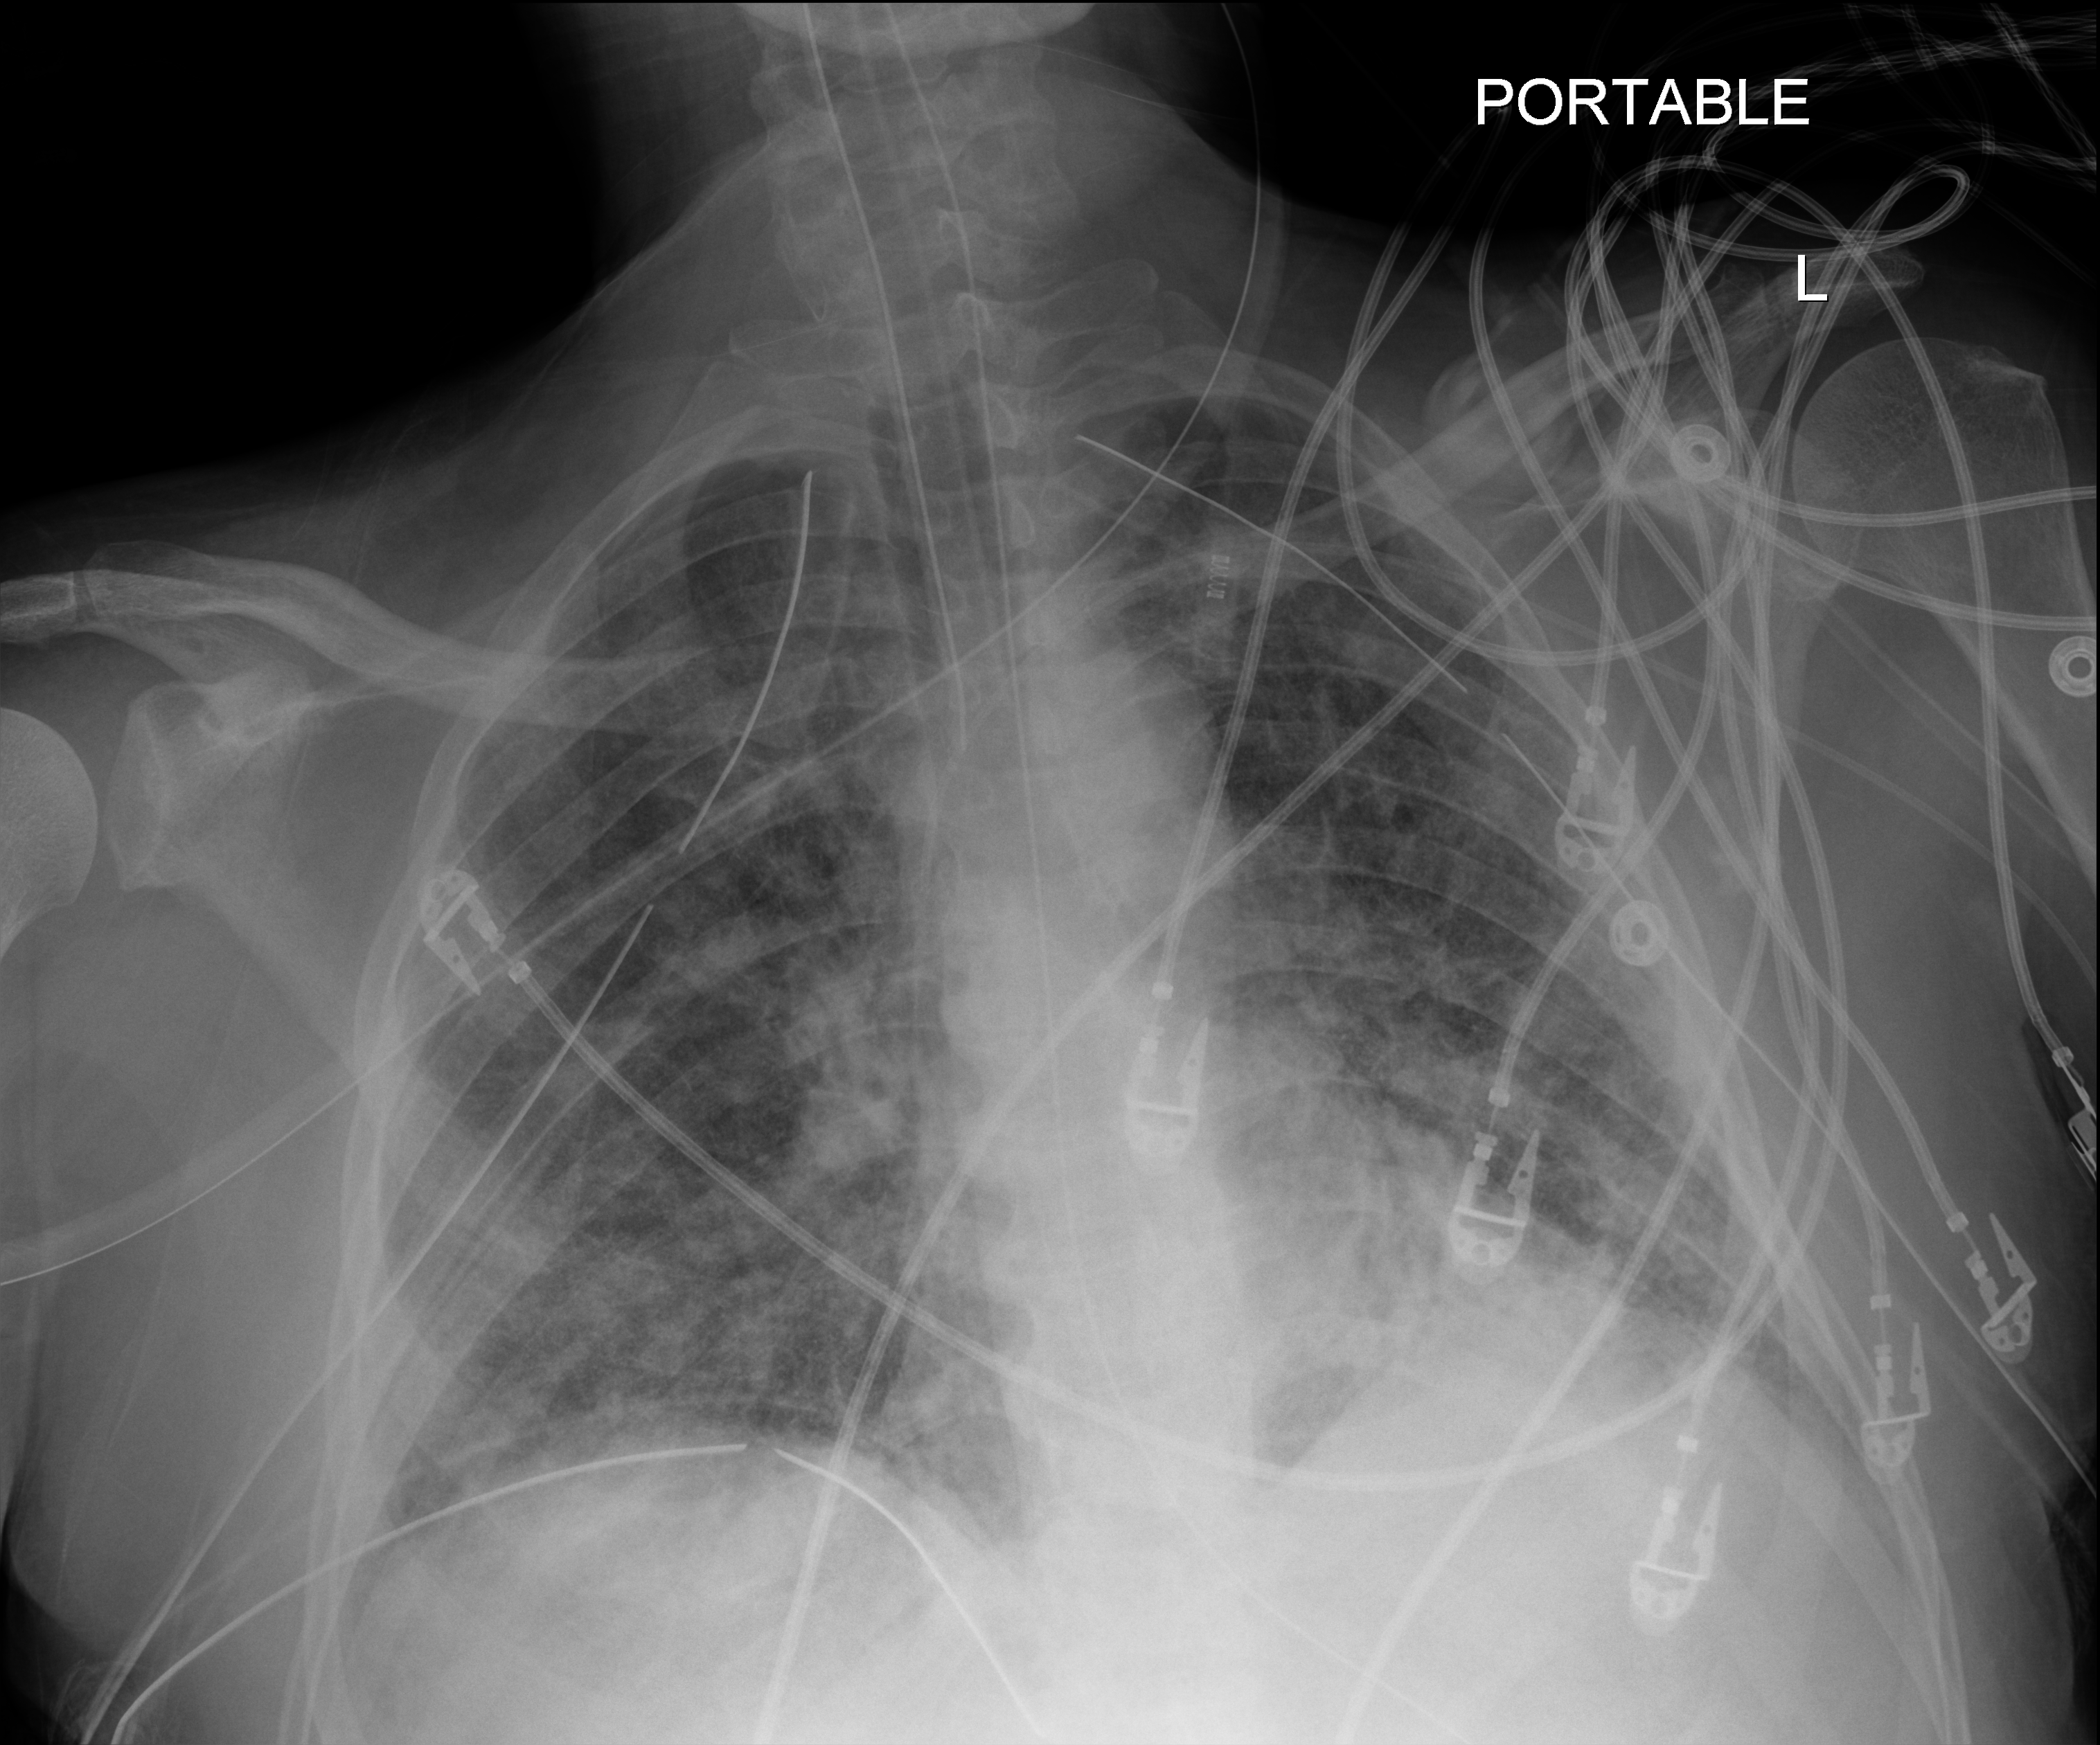
Bedside chest radiograph (digital radiography); anteroposterior (AP) projection. Male patient hospitalised with COVID-19, age 18–59 years.
Admission-level facts for this patient (not findings on this image; timing relative to this image not recorded):
- mechanically ventilated during this hospital stay: yes
- admitted to intensive care during this hospital stay: yes
- length of hospital stay: 83 days